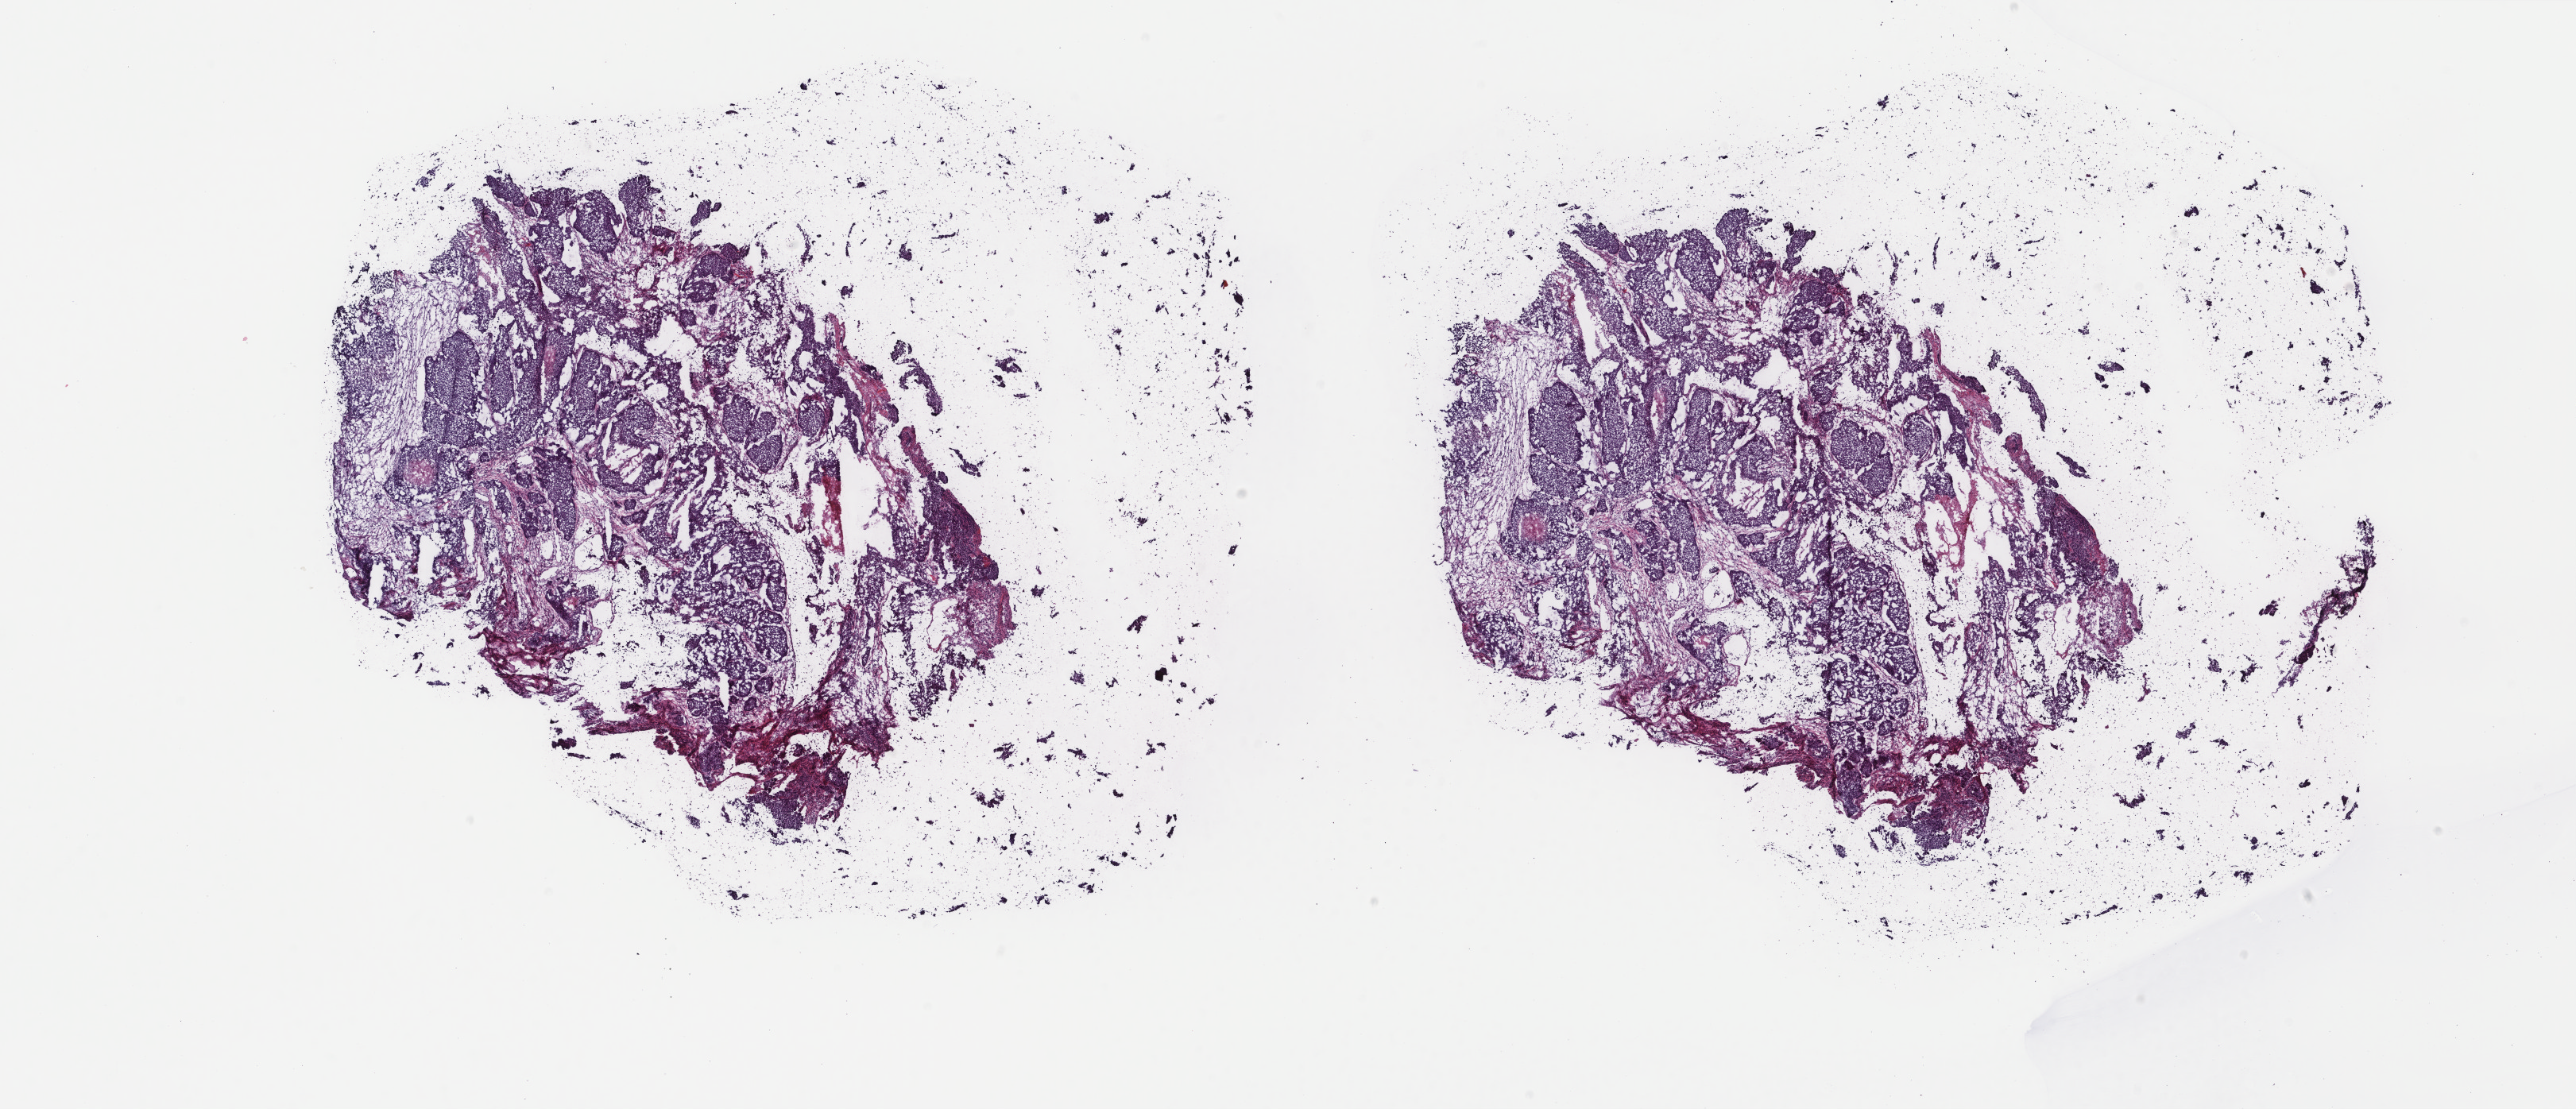
H&E whole-slide image — low-resolution overview of the scanned area, about 25.7 x 11.1 mm (acquisition: 40x scan); frozen section from the bottom of the tissue portion; breast, primary tumour sample. Female, age 38 years at initial diagnosis. Slide review estimates, as recorded: tumour cells 75%, tumour nuclei 75%.
Diagnosis: Infiltrating duct mixed with other types of carcinoma.